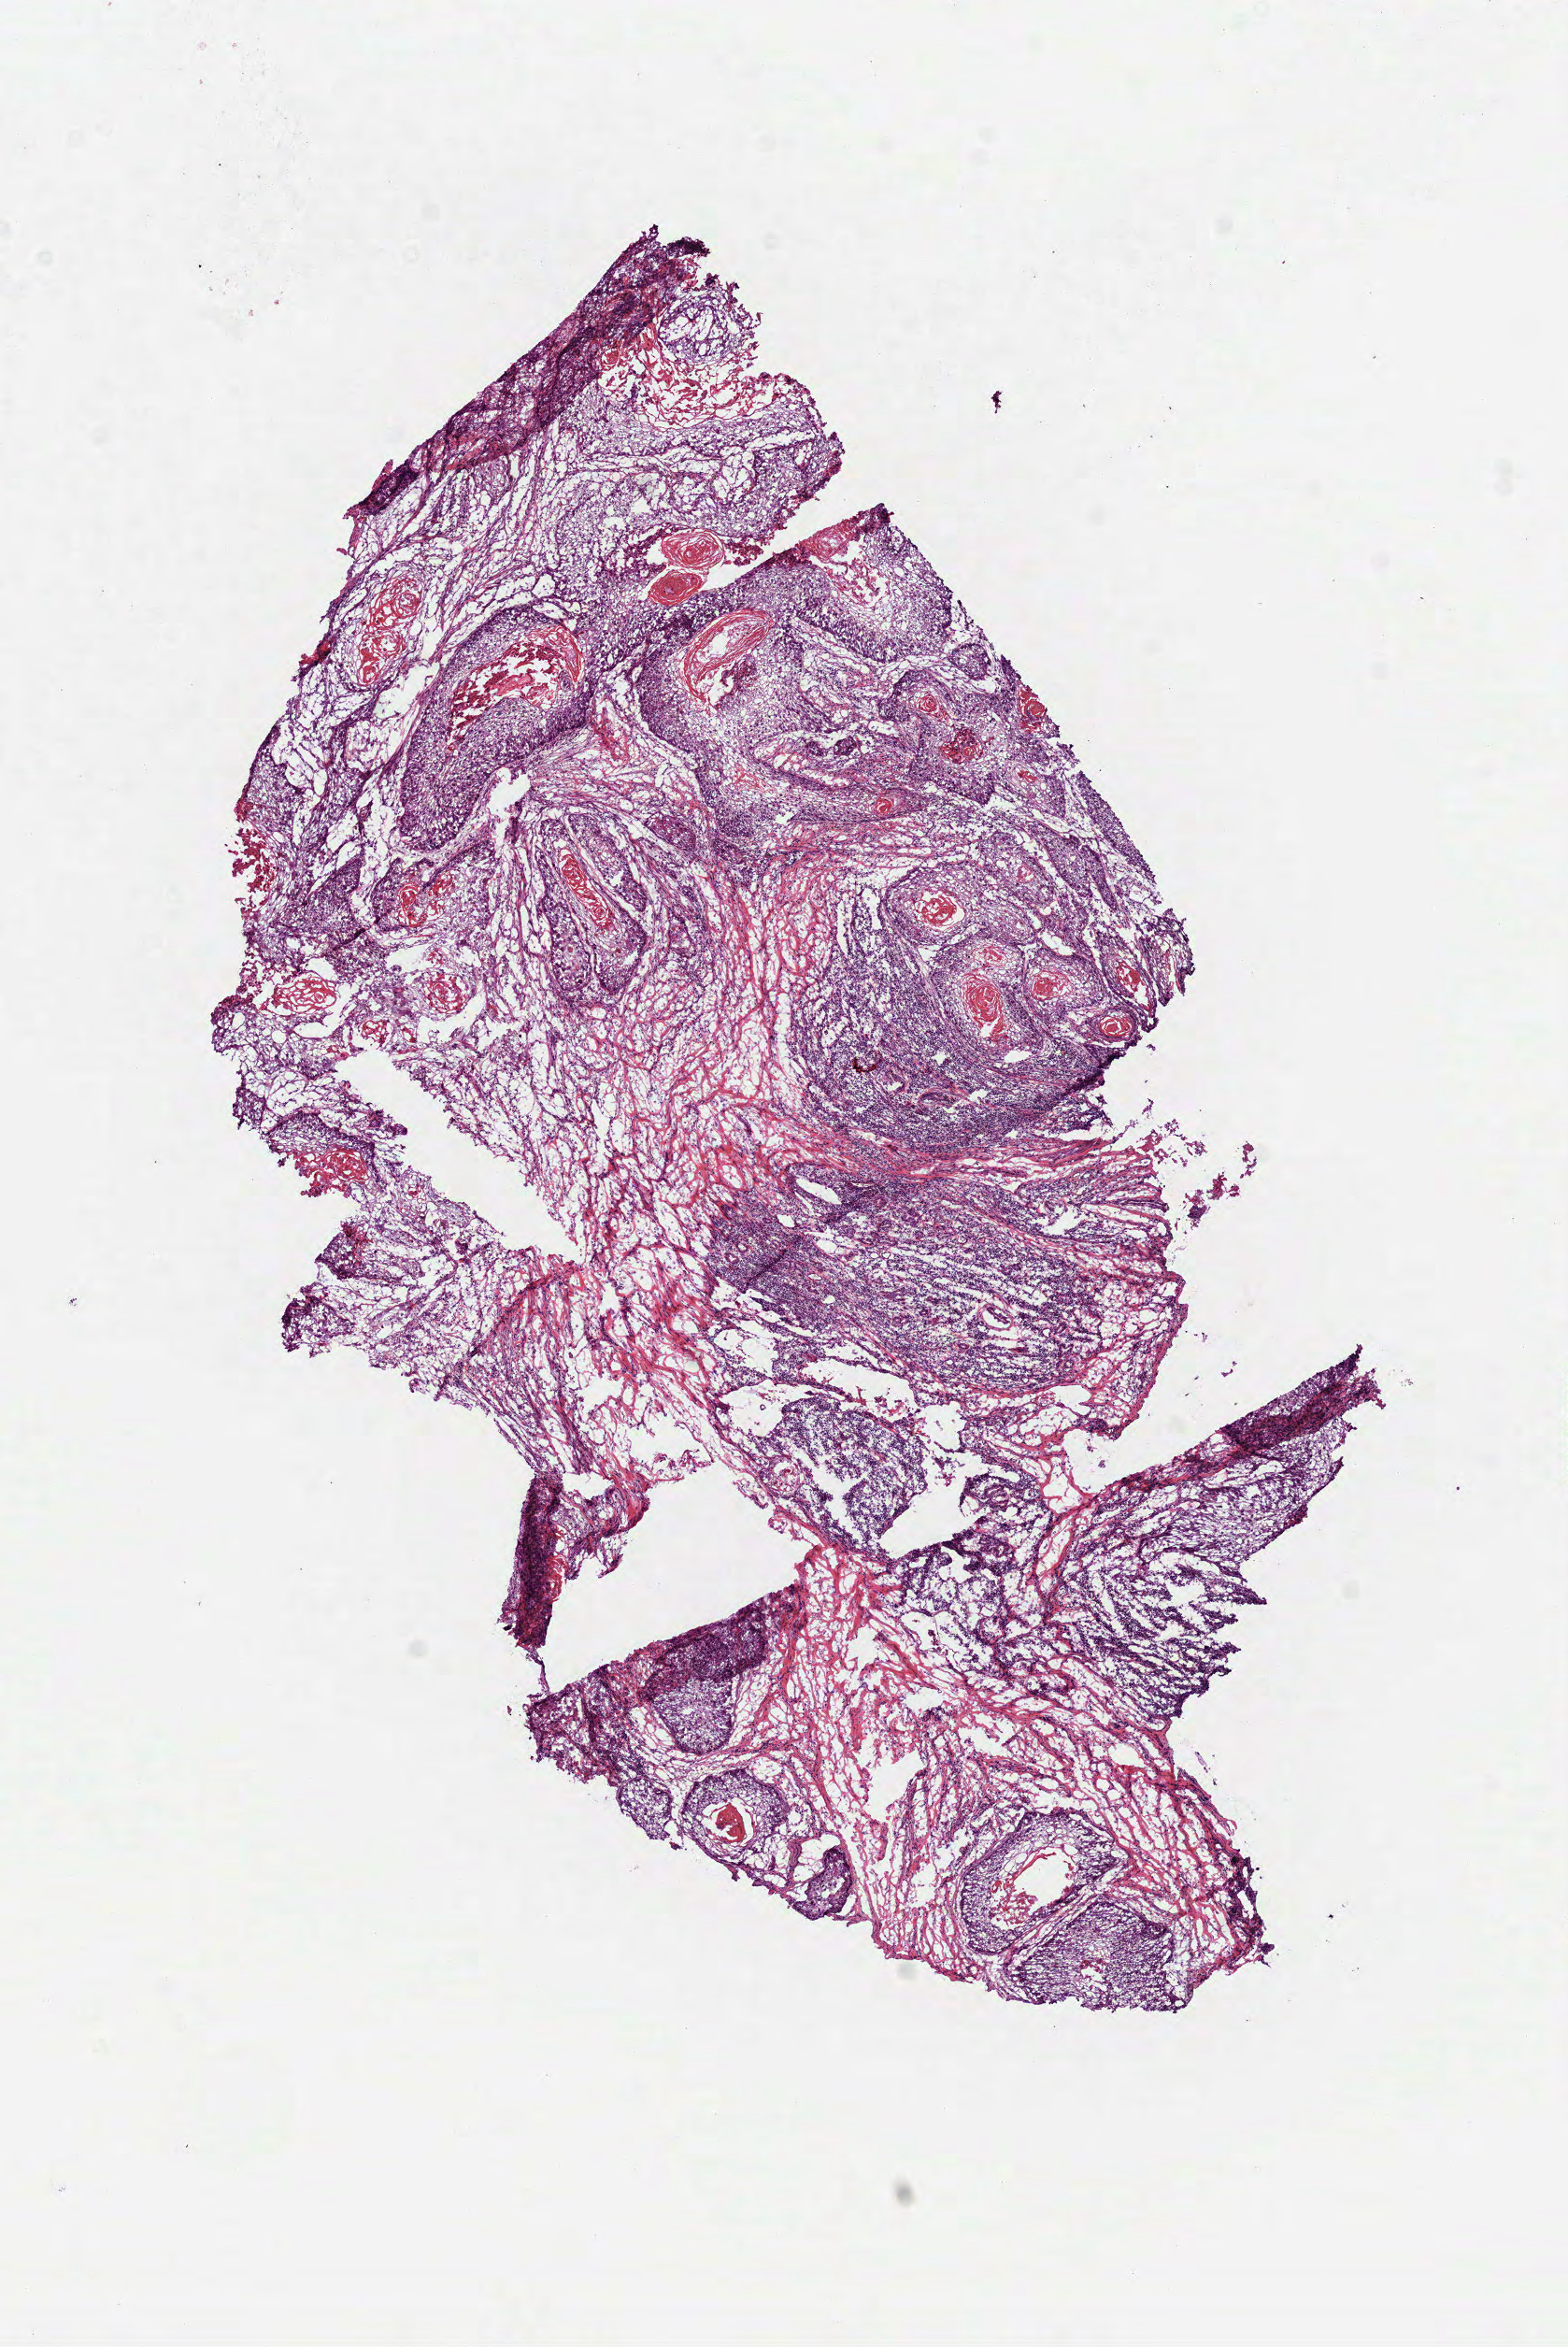
Hematoxylin and eosin (H&E) stained whole-slide image — whole scanned area (about 6.8 x 10.1 mm, acquisition: 40x scan) shown as a low-resolution overview; frozen section from the bottom of the tissue portion; primary tumour sample from the head and neck. Male patient; age at initial diagnosis 51 years. Histologic grade: G2 (moderately differentiated). Pathologist review of this section (percent, as recorded): tumour cells 70%, tumour nuclei 60%, normal cells 0%, stromal cells 25%, necrosis 5%. Infiltration values recorded for this section: lymphocyte infiltration 30%.
- histologic diagnosis: Squamous cell carcinoma, NOS (tongue, NOS)
- lymph nodes positive (case pathology): 0 of 29 examined
- AJCC pathologic stage: III